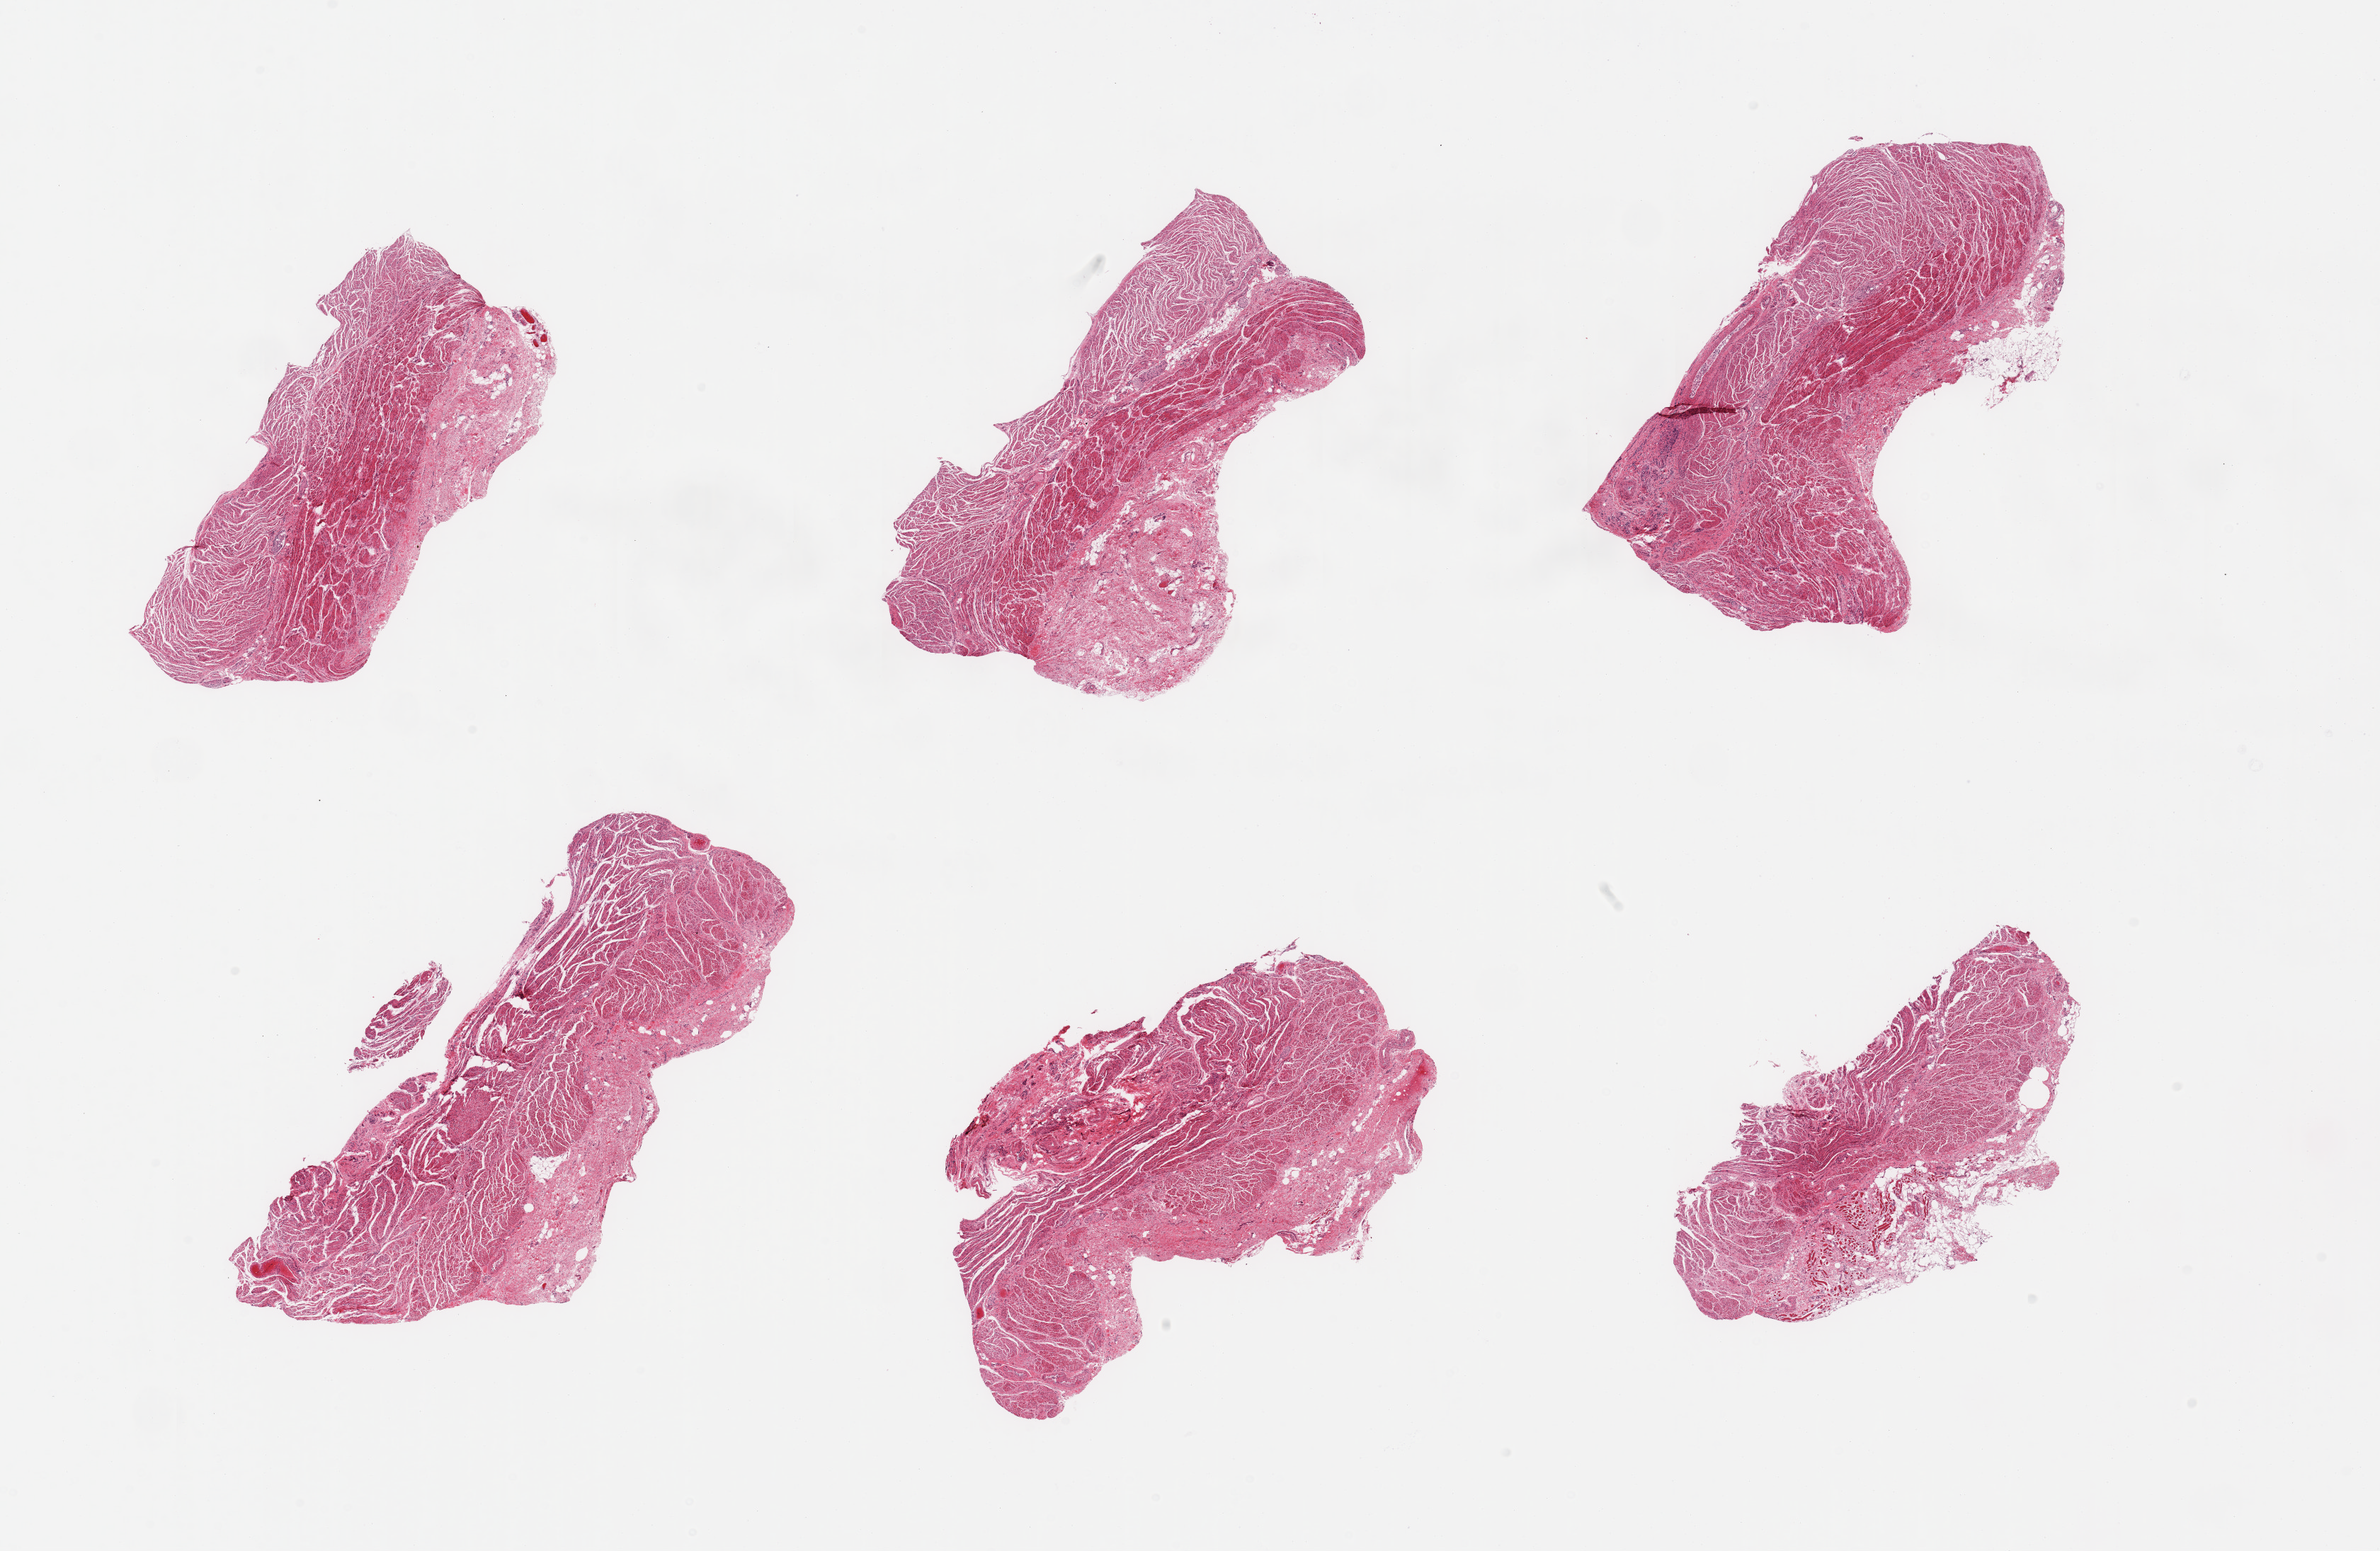
Whole-slide image, H&E stain, low-resolution overview of the scanned area, about 26.6 x 17.3 mm (acquisition: 20x scan), PAXgene-fixed, paraffin-embedded tissue, sampled site (target tissue): gastroesophageal junction, tissue donor sample. Donor sex: female.
* reviewer comment on this tissue sample: 6 pieces; submucosal stroma comprises up to 40%